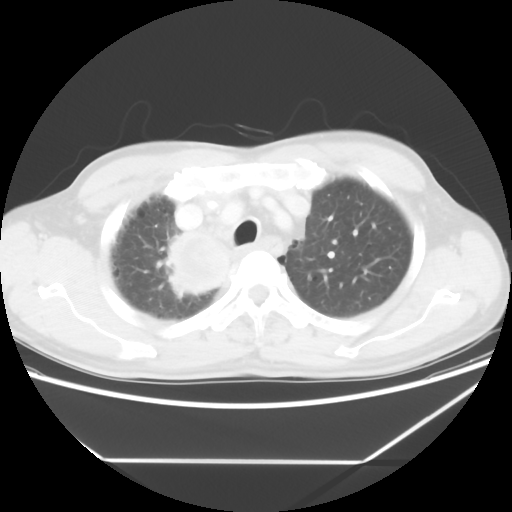
Chest CT, one axial slice. Position 49 of 60 along the scan axis. 120 kVp. Lung window (W 1500 / L -600 HU). 5 mm slice thickness. 512 × 512 image matrix, field of view 367 × 367 mm. Patient: male, 58 years. From the clinical record (not read from this slice): clinical TNM (as recorded): T2 N2 M0.
Structures marked on this image (rectangle marked by the reading radiologist):
- lung tumour (recorded histology: squamous cell carcinoma): bounding box <149,217,244,296> (left, top, right, bottom; pixels)